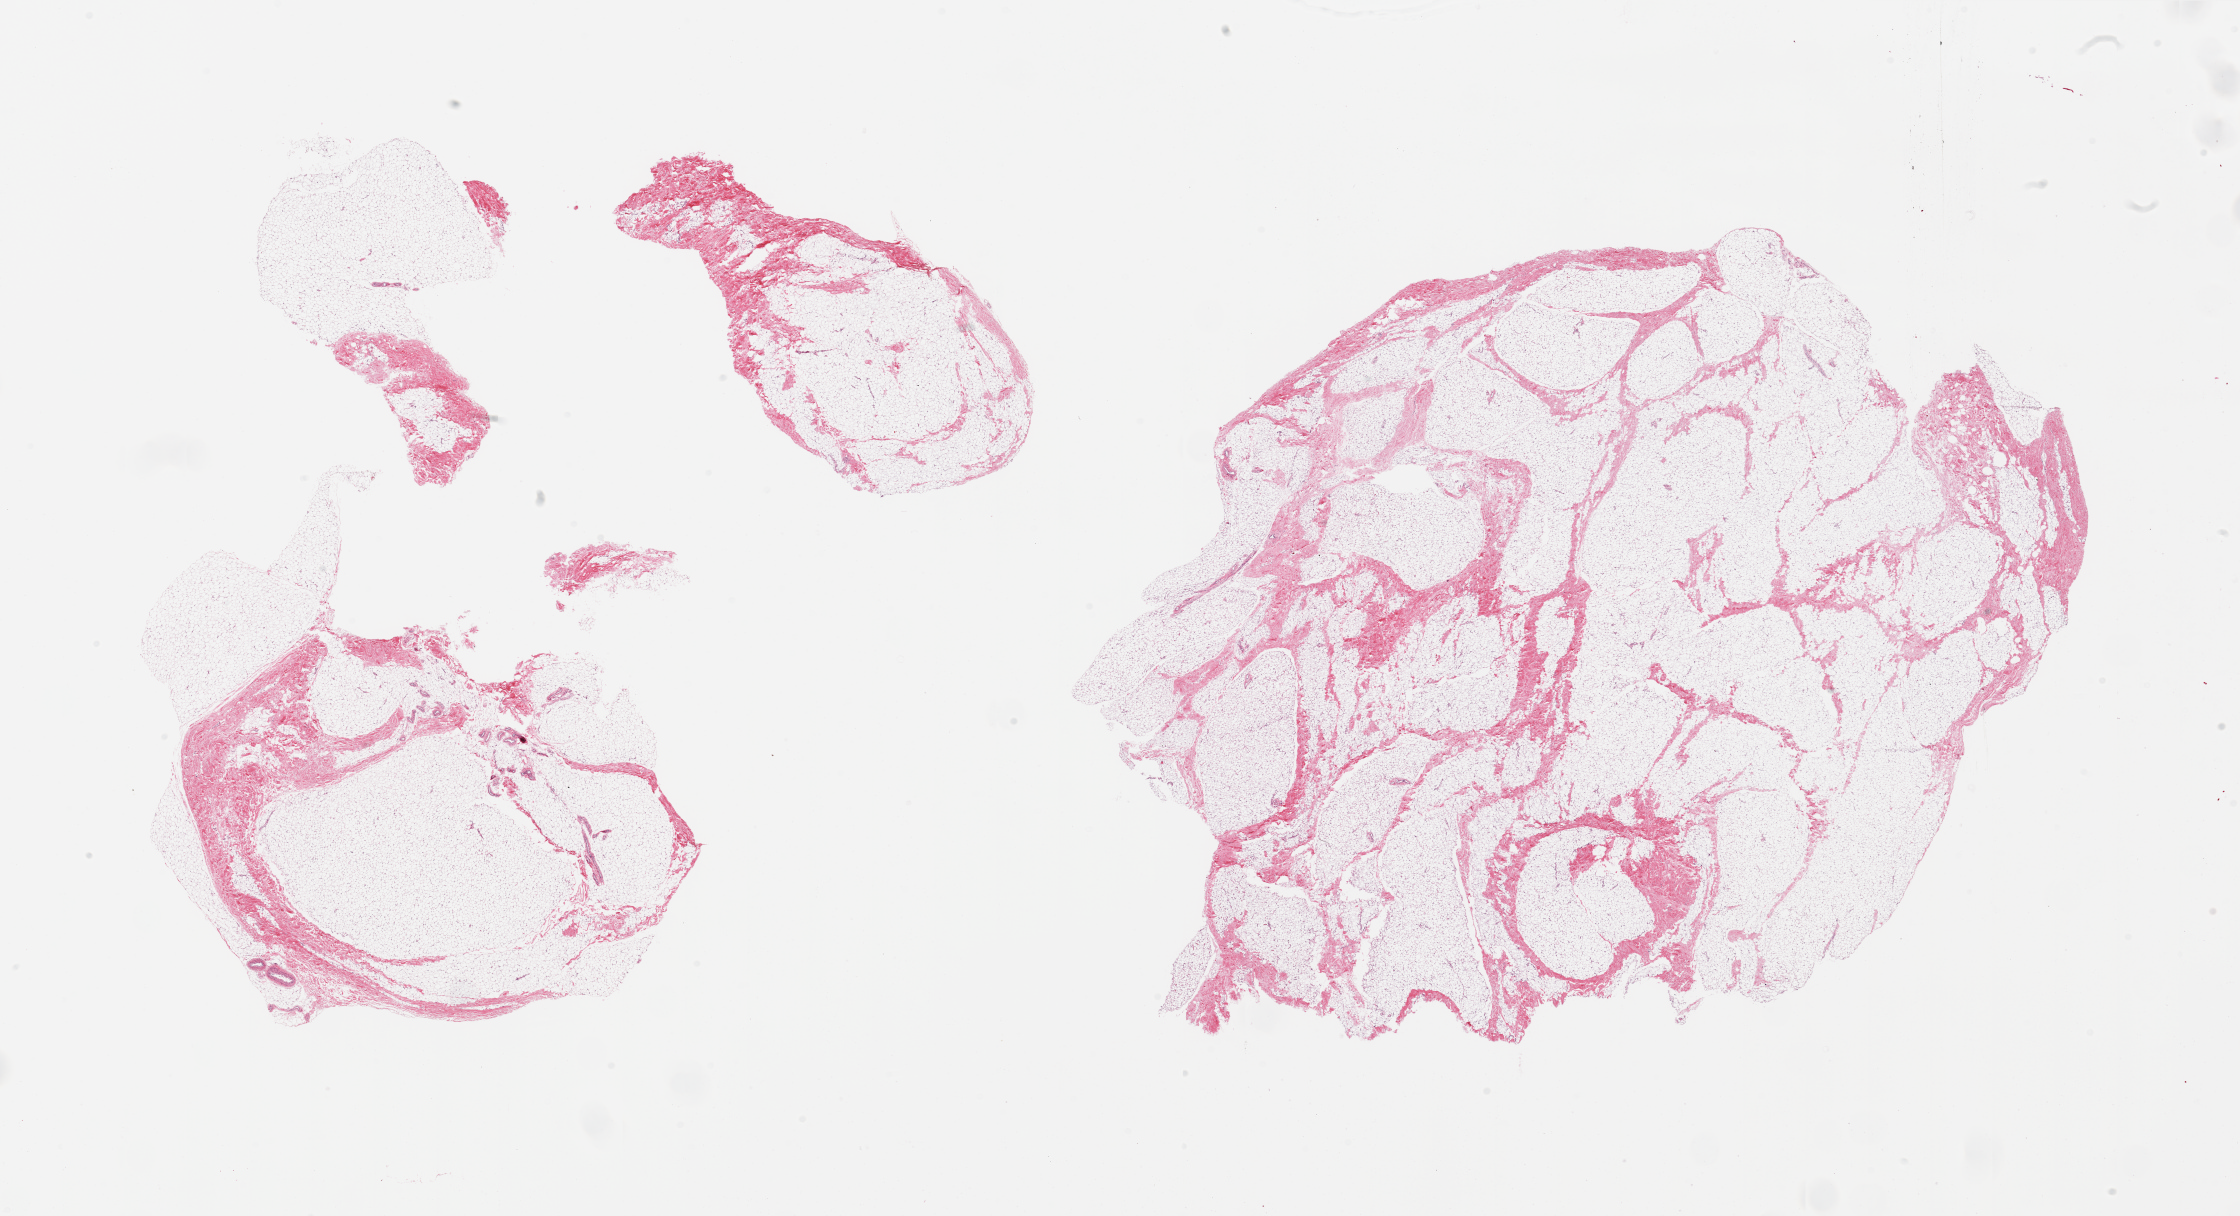
Whole-slide image, H&E stain, brightfield — a low-resolution overview of the entire scanned area, about 35.4 x 19.2 mm; PAXgene-fixed, paraffin-embedded tissue; target tissue: breast; tissue donor sample. Donor: male.
Pathologist's review note for this sample: 2 pieces, fiboradipose tissue, no ductal elements noted.